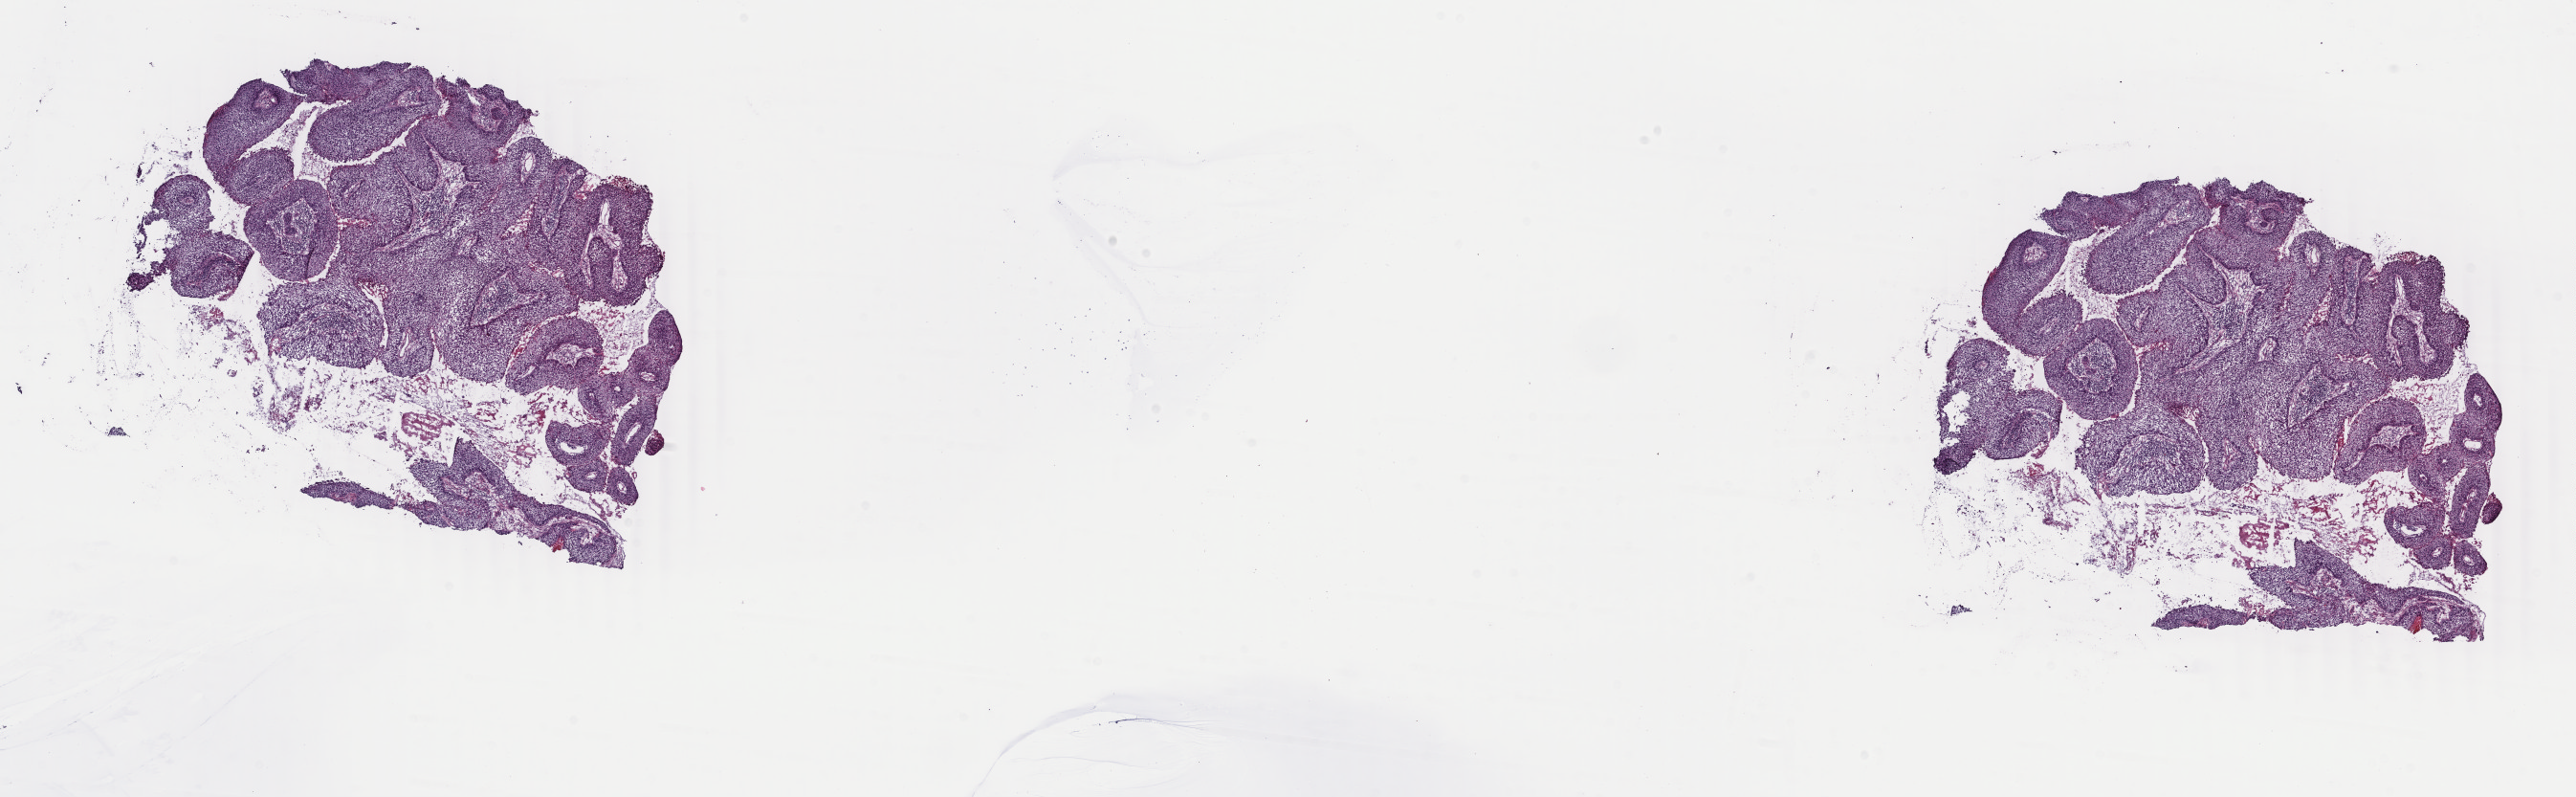
H&E-stained whole-slide image, shown as a low-resolution overview of the whole scanned area (about 21.4 x 6.6 mm), frozen section from the top of the tissue portion, primary tumour sample from the lung. Patient: male, age at initial diagnosis 77 years. Composition of this section per pathologist review: tumour cells 100%, tumour nuclei 90%, normal cells 0%, stromal cells 0%, necrosis 0%. Infiltration values recorded for this section: lymphocyte infiltration 0%, monocyte infiltration 0%, neutrophil infiltration 0%.
AJCC pathologic stage: IIA. Pathologic diagnosis: Squamous cell carcinoma, NOS (lower lobe, lung).